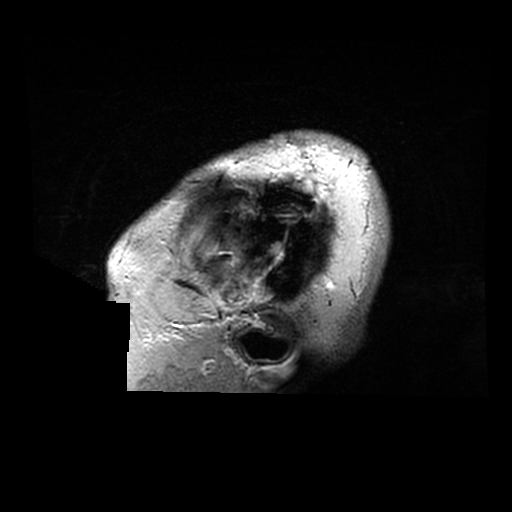
Brain MRI from a brain-tumour surgery series, one sagittal slice; slice 267 of 320 in the series (ordered by position); 512 × 512 image matrix, field of view 240 × 240 mm. Case-level facts recorded for this patient, not image findings: histopathology: Astrocytoma; WHO grade: 2; IDH mutation: yes.
Annotated regions visible in this slice (manually delineated by an expert):
- tumour: bounding box (x1, y1, x2, y2) in pixels: (274, 245, 281, 263)